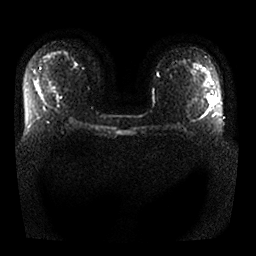
Breast MRI, one axial slice. Diffusion-weighted series; image 2 of 4 stored at this slice position (different b-values; order by instance number). 1.5 T. 256 × 256 image matrix. Female patient.
Structures marked on this image (expert manual segmentation):
- tumour on diffusion-weighted imaging: bounding box [x1, y1, x2, y2] px = [210, 97, 215, 102]